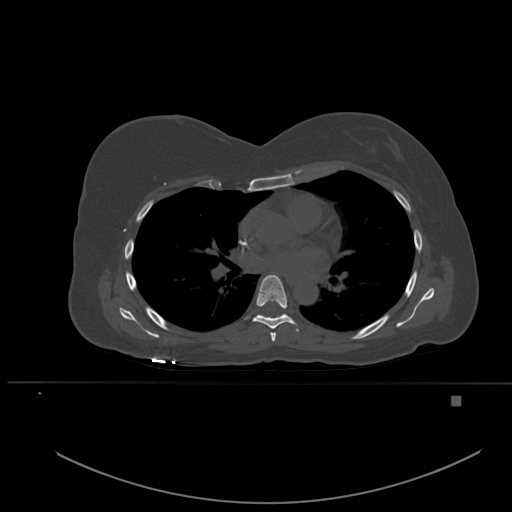
CT including the spine, one axial slice. Position 350 of 651 along the scan axis. Bone window (W 1800 / L 400 HU). 1.5 mm slice thickness. 512 × 512 image matrix, field of view 443 × 443 mm. Patient: female, 49 years. From the clinical record (not read from this slice): primary cancer: breast; vertebrae with lytic lesions (as recorded): L3, T12, L4.
Structures marked on this image (semi-automatically segmented with operator editing):
- T5 vertebra: box from (x=270, y=332) to (x=276, y=342) px
- T6 vertebra: (x=252, y=275)–(x=299, y=332)